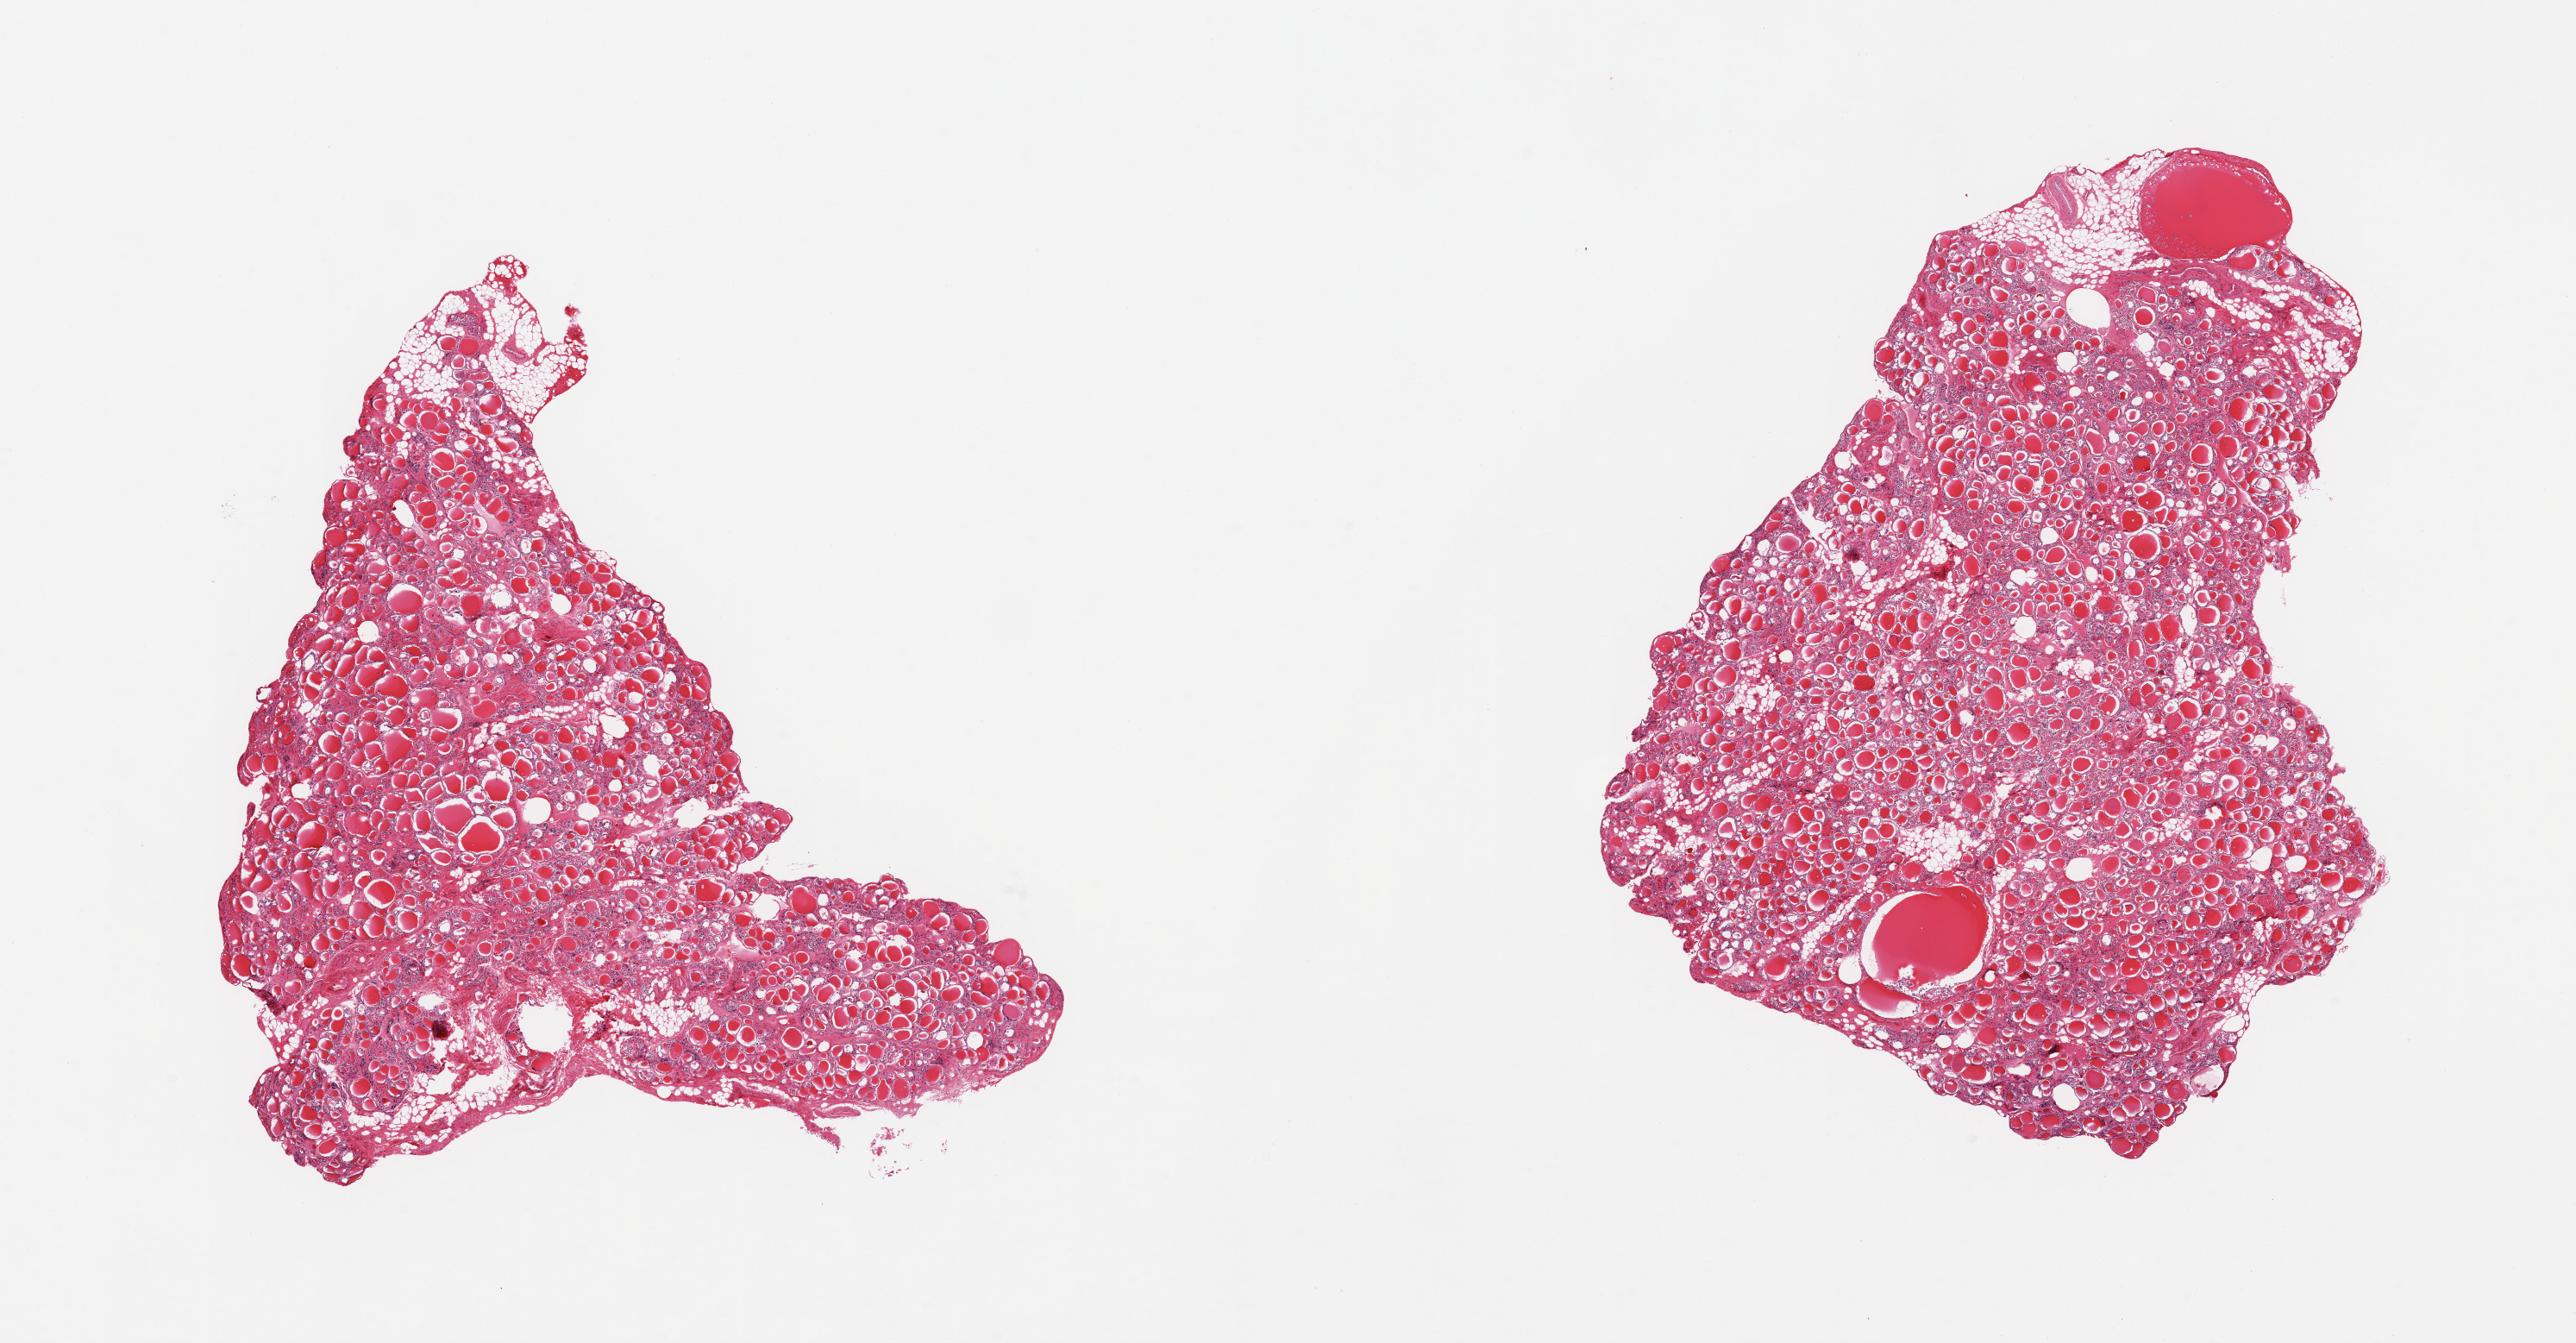
Haematoxylin and eosin whole-slide image, brightfield, whole scanned area (about 23.6 x 12.3 mm) shown as a low-resolution overview, PAXgene-fixed, paraffin-embedded tissue, section of thyroid (target tissue), tissue donor sample. Donor sex: male.
- pathologist's review note for this sample: 2 pieces; 10% internal fat content